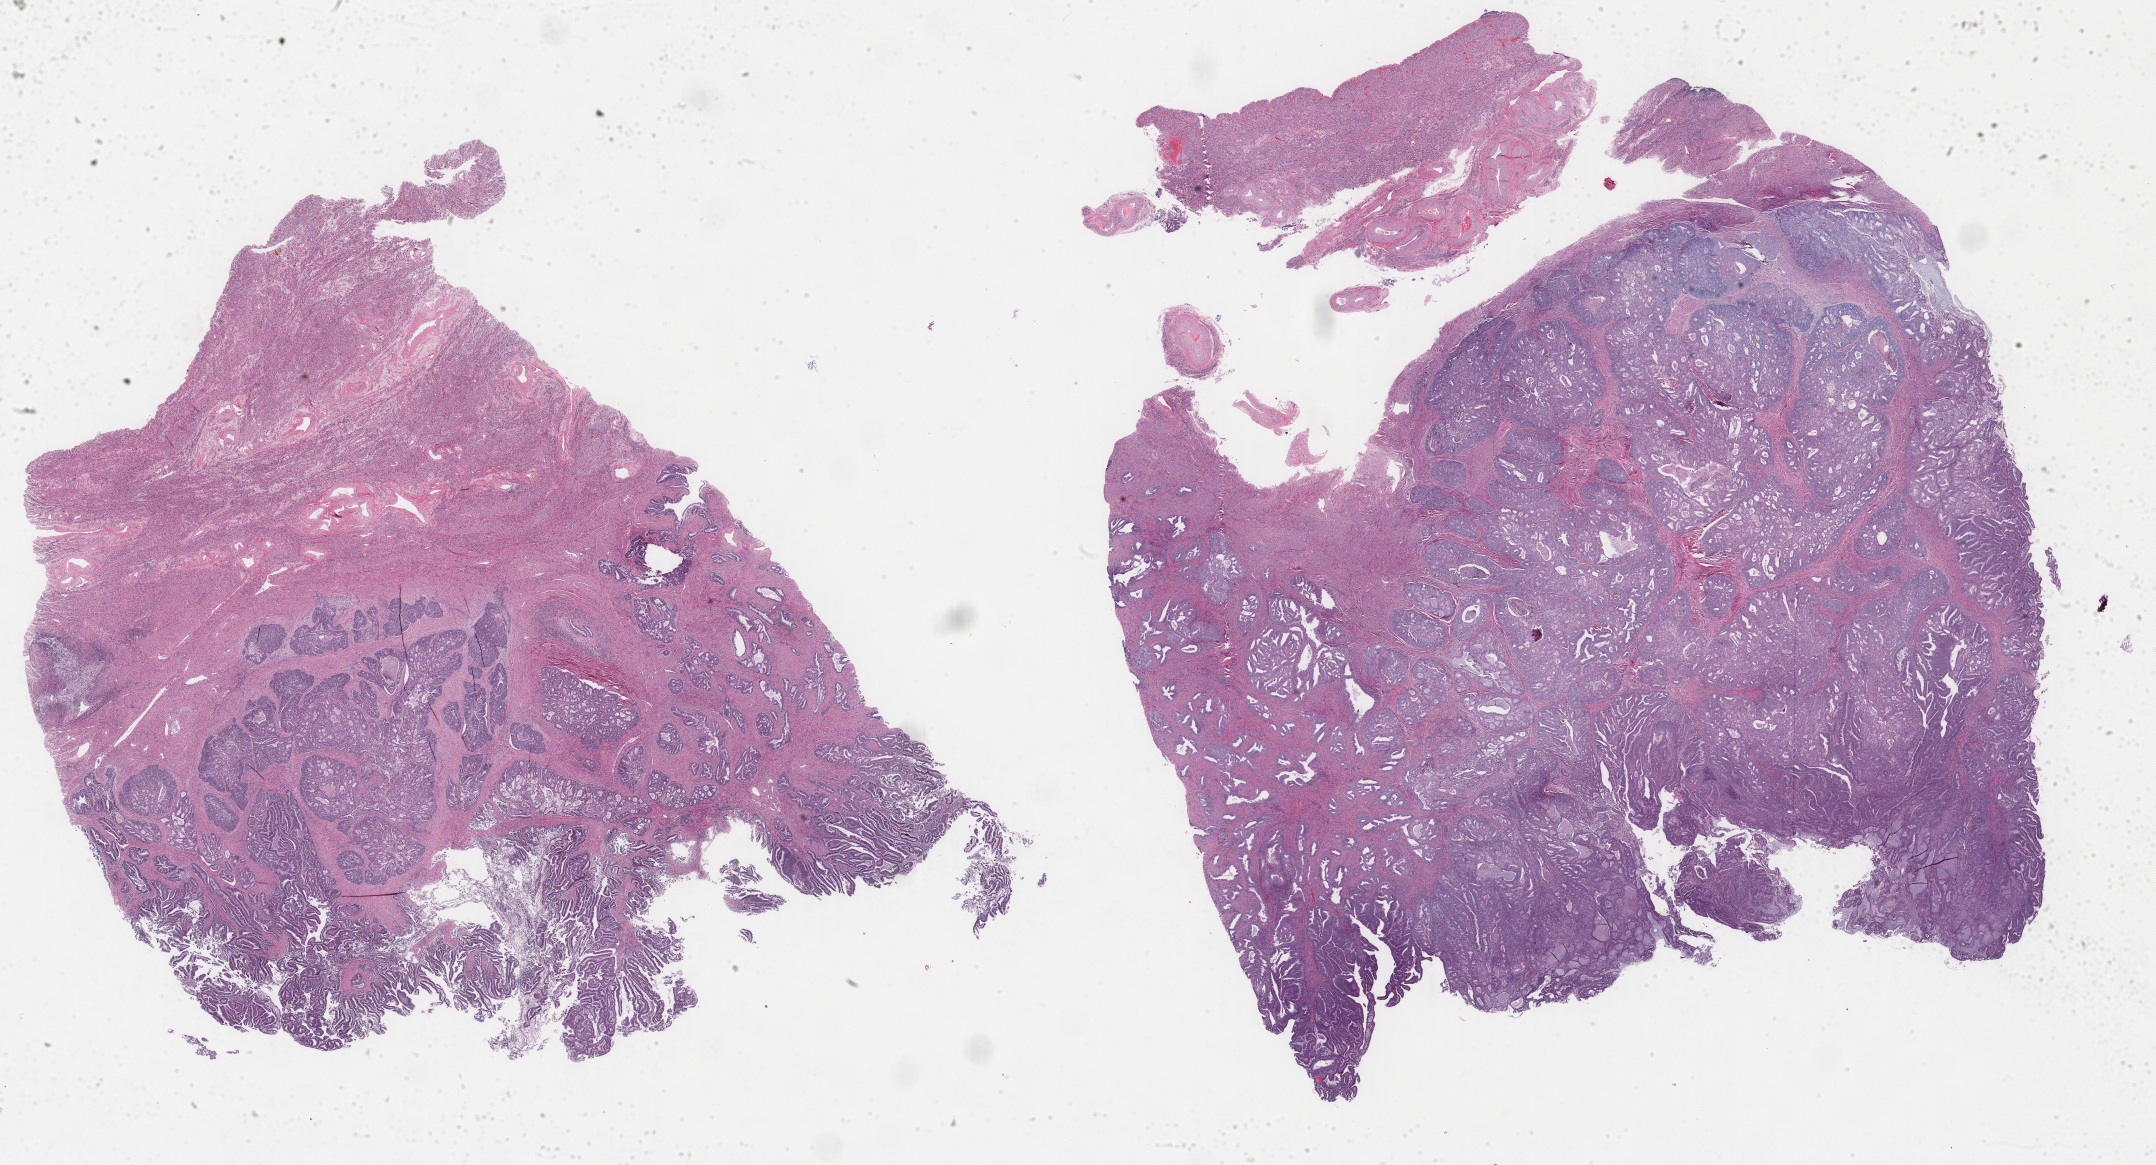
Digitized Hematoxylin and eosin (H&E) stained tissue section (whole slide) — low-resolution overview of the scanned area, about 34.2 x 18.5 mm, formalin-fixed paraffin-embedded (FFPE) diagnostic section, sample: primary tumour, uterus. Female patient; age at initial diagnosis 69 years. Histologic grade: G1 (well differentiated).
• histologic diagnosis: Endometrioid adenocarcinoma, NOS (endometrium)
• FIGO stage: IB
• lymph nodes positive (case pathology): 0 of 16 examined